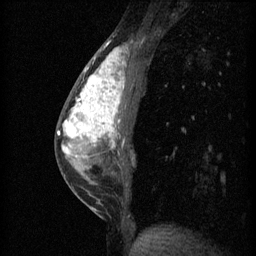
Breast MRI (dynamic contrast-enhanced), one sagittal slice; position 23 of 60 along the scan axis; 3 images stored at this slice position (order not interpretable as contrast timing); 1.5 T; TE 4.2 ms, TR 11 ms; 2 mm slice thickness; 256 × 256 image matrix, field of view 180 × 180 mm. Female patient, age 40 years.
Annotated regions visible in this slice (semi-automatically segmented with operator editing):
- analysis volume of interest (the breast-tissue region the enhancement analysis was run in; not a lesion): box from (x=56, y=42) to (x=139, y=203) px
- tumour enhancement mask (voxels above the 70 % enhancement threshold inside the analysis volume of interest): (x=58, y=48)–(x=126, y=159)